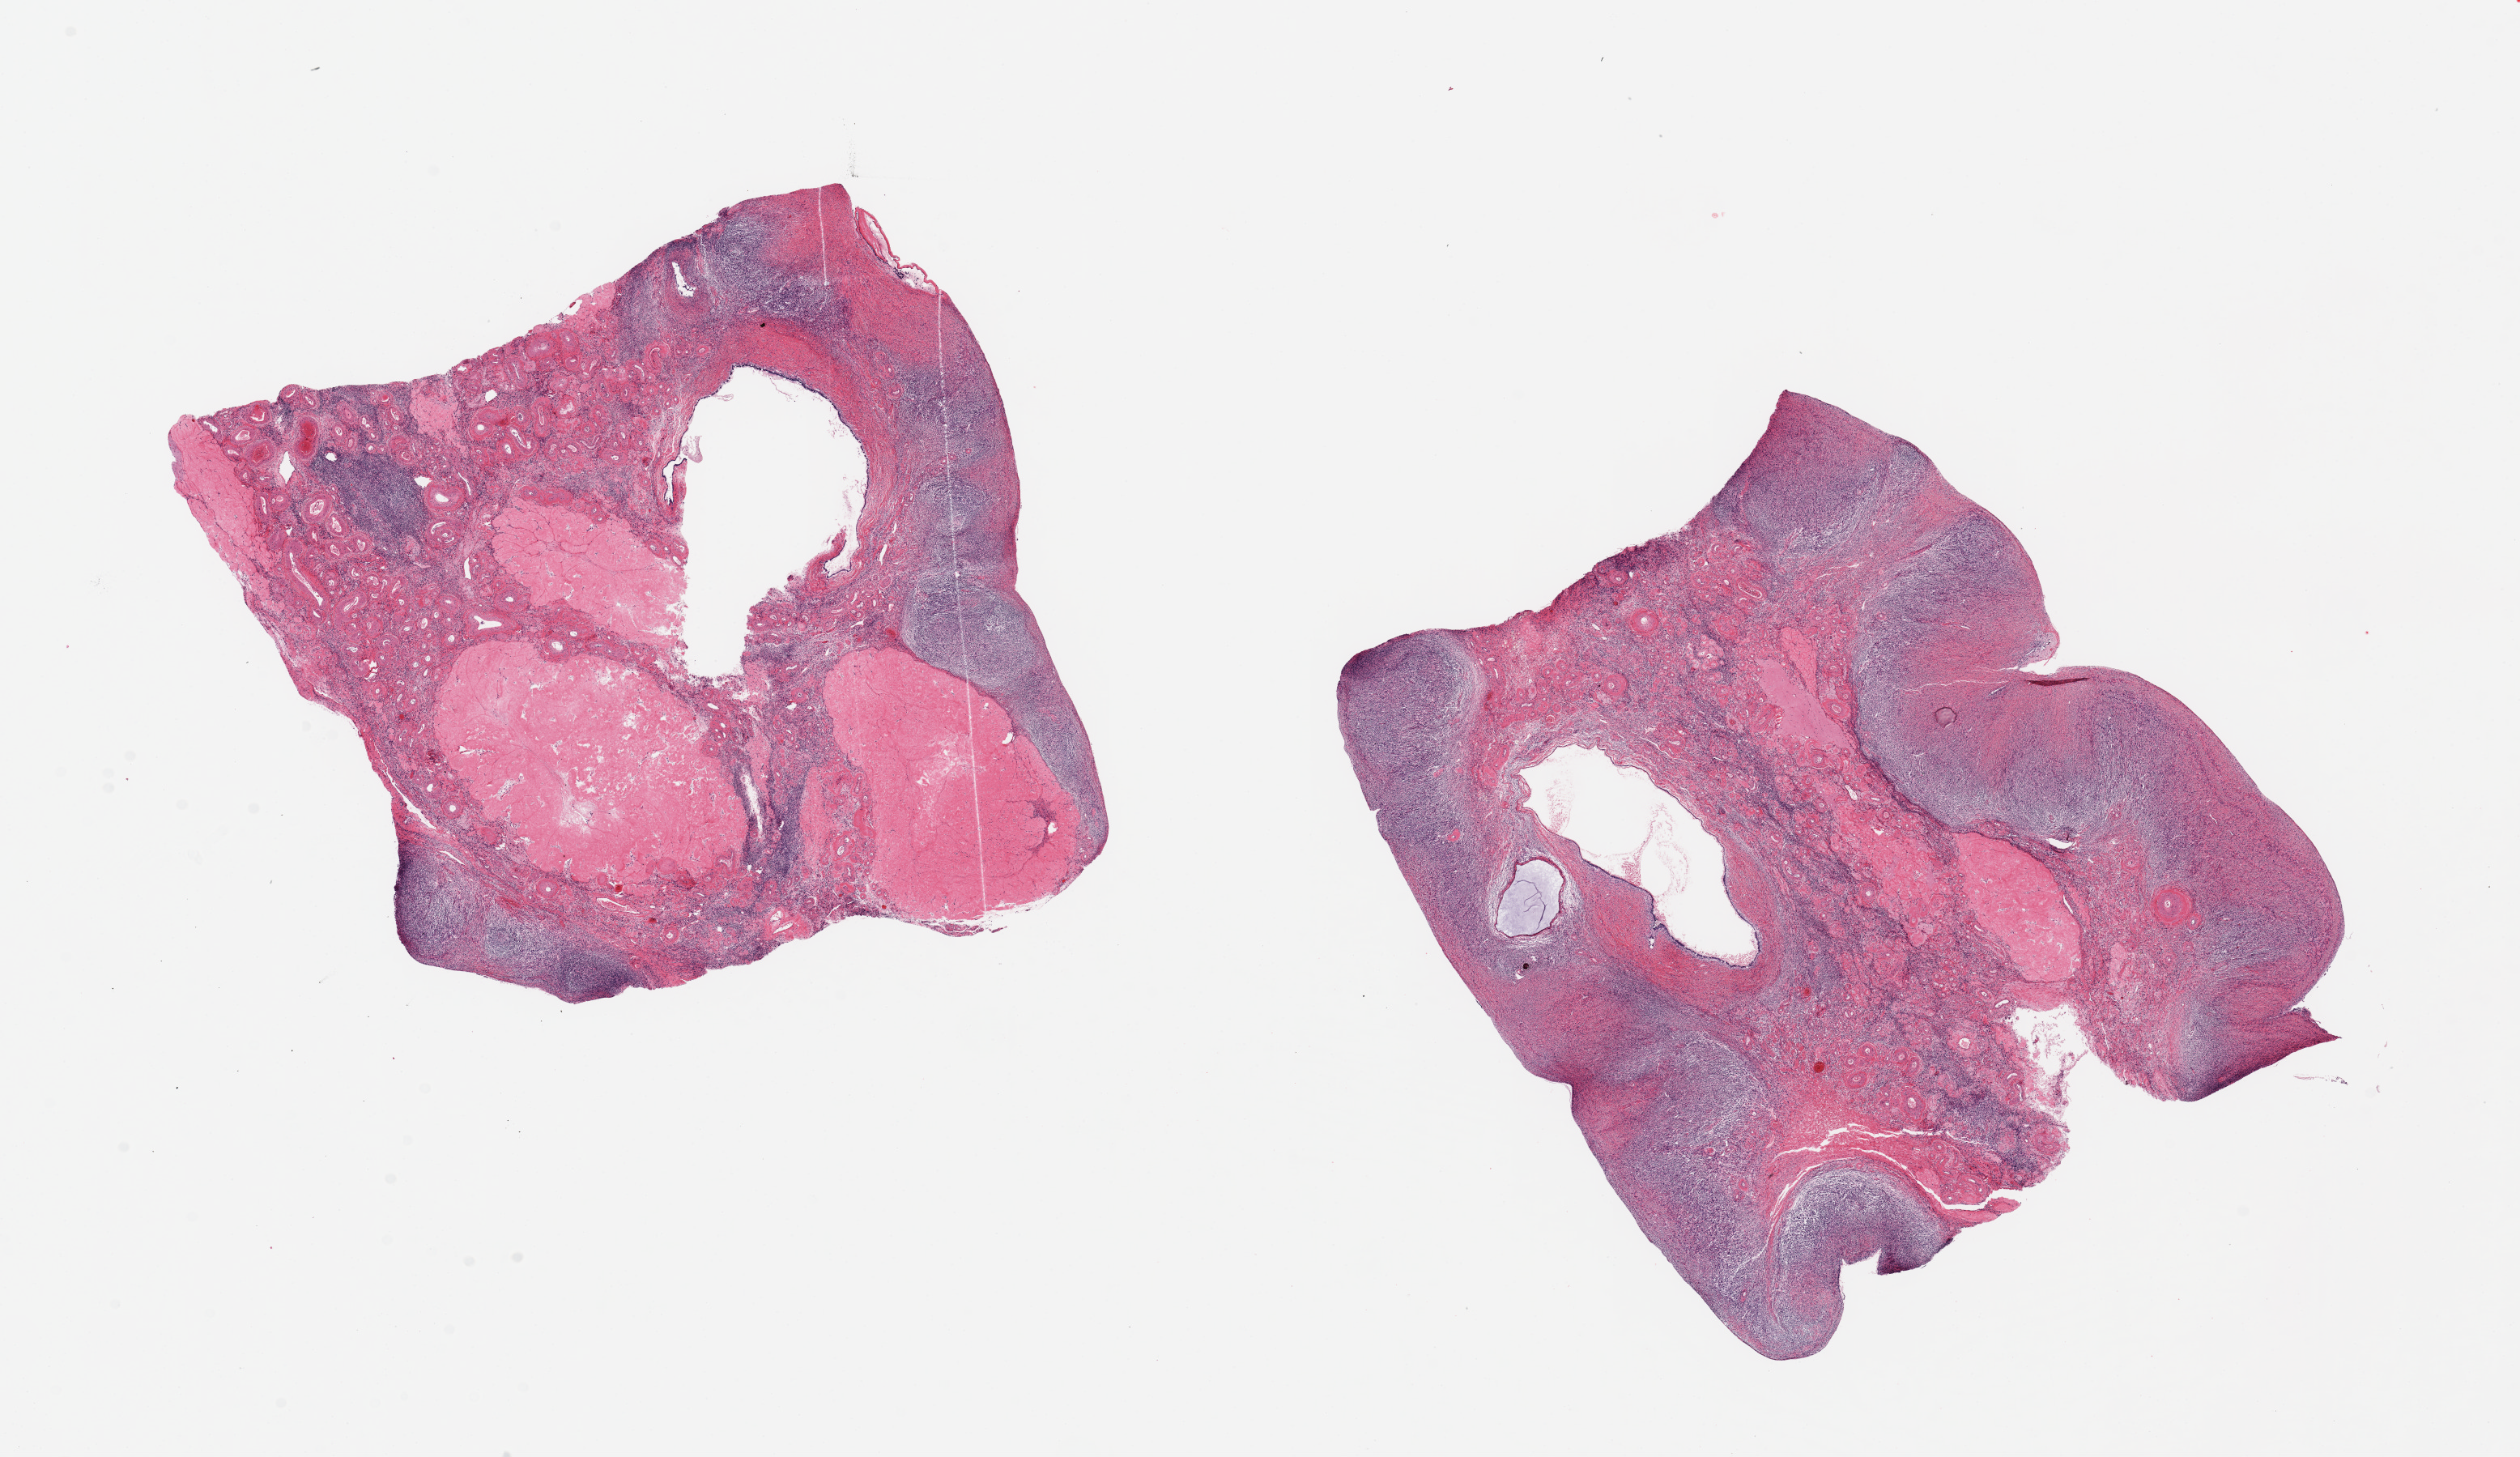
Digitized H&E-stained section, shown as a low-resolution overview of the whole scanned area (about 24.6 x 14.2 mm, slide scanned at 20x); PAXgene-fixed, paraffin-embedded tissue; target tissue: ovary; tissue donor sample. Female donor.
Reviewer comment on this tissue sample: 2 pieces, 7x7 & 8x7mm; large corpora albicantia.